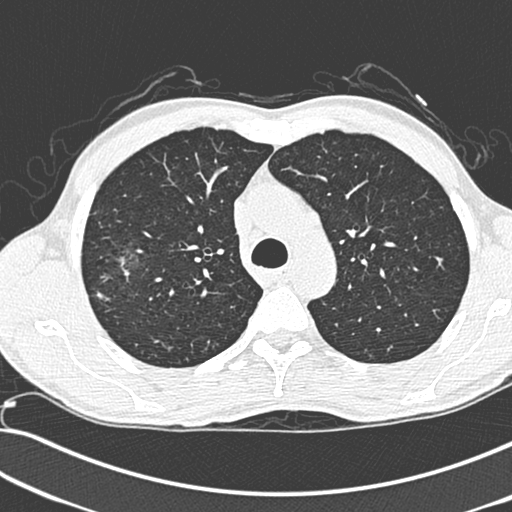
Low-dose screening chest CT, one axial slice. Position 213 of 281 along the scan axis. 120 kVp. Lung window (W 1500 / L -600 HU). 1.3 mm slice thickness. 512 × 512 image matrix.
Annotated regions visible in this slice (expert manual segmentation):
- lesion 1 (tumor, upper lobe of right lung): bounding box <119,257,130,281> (left, top, right, bottom; pixels)